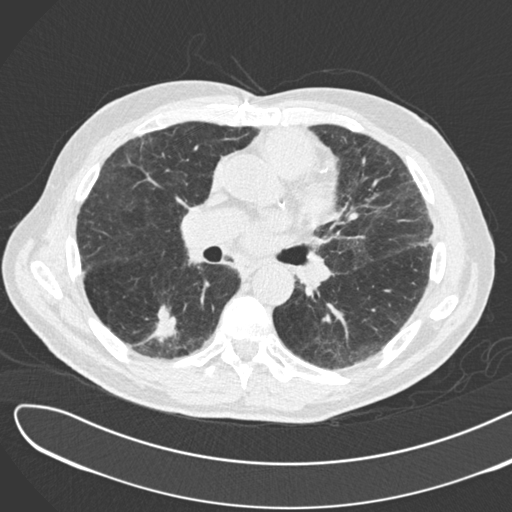
Low-dose screening chest CT, one axial slice; position 92 of 183 along the scan axis; reconstruction kernel B30f; lung window (W 1500 / L -600 HU); 2 mm slice thickness; 512 × 512 image matrix.
Structures marked on this image (expert manual segmentation):
- lesion 1 (tumor, lower lobe of right lung): bounding box [x1, y1, x2, y2] px = [152, 305, 178, 343]